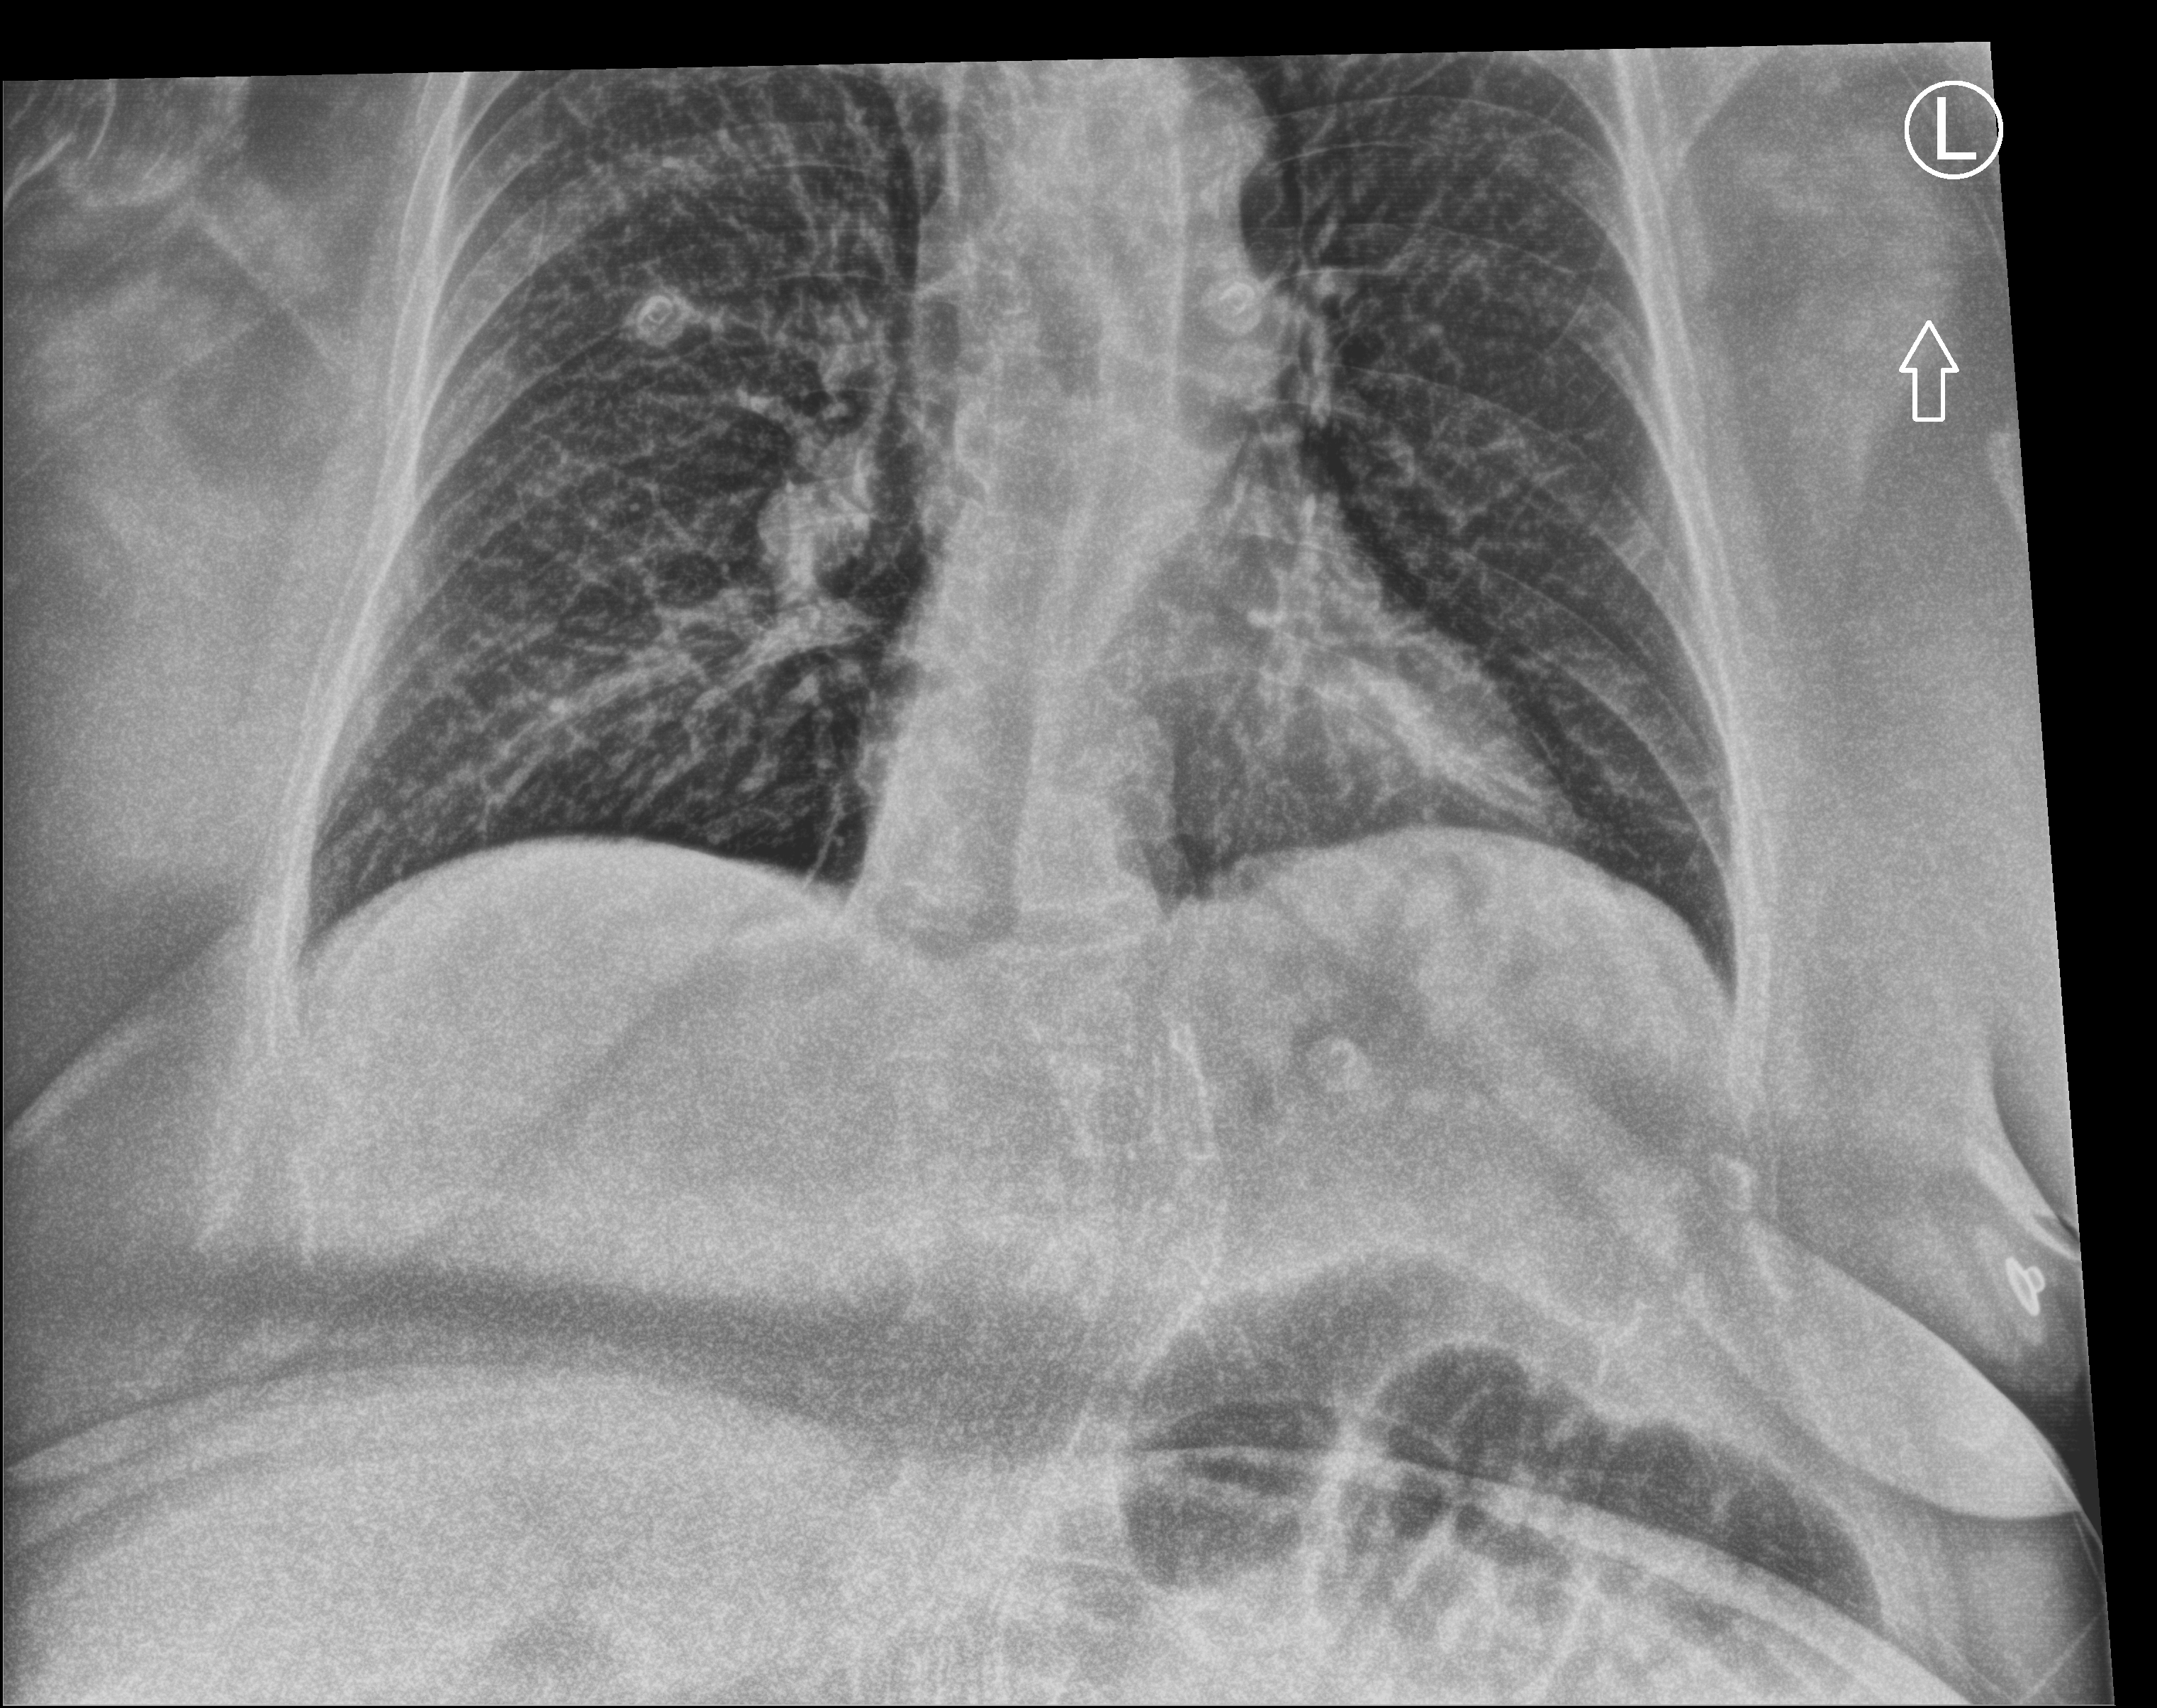
Portable abdomen radiograph, anteroposterior (AP) projection. Female patient hospitalised with COVID-19, age 60–74 years.
Hospital-stay facts (about this admission, not read from this image; timing relative to this image not recorded): mechanically ventilated during this hospital stay: no.